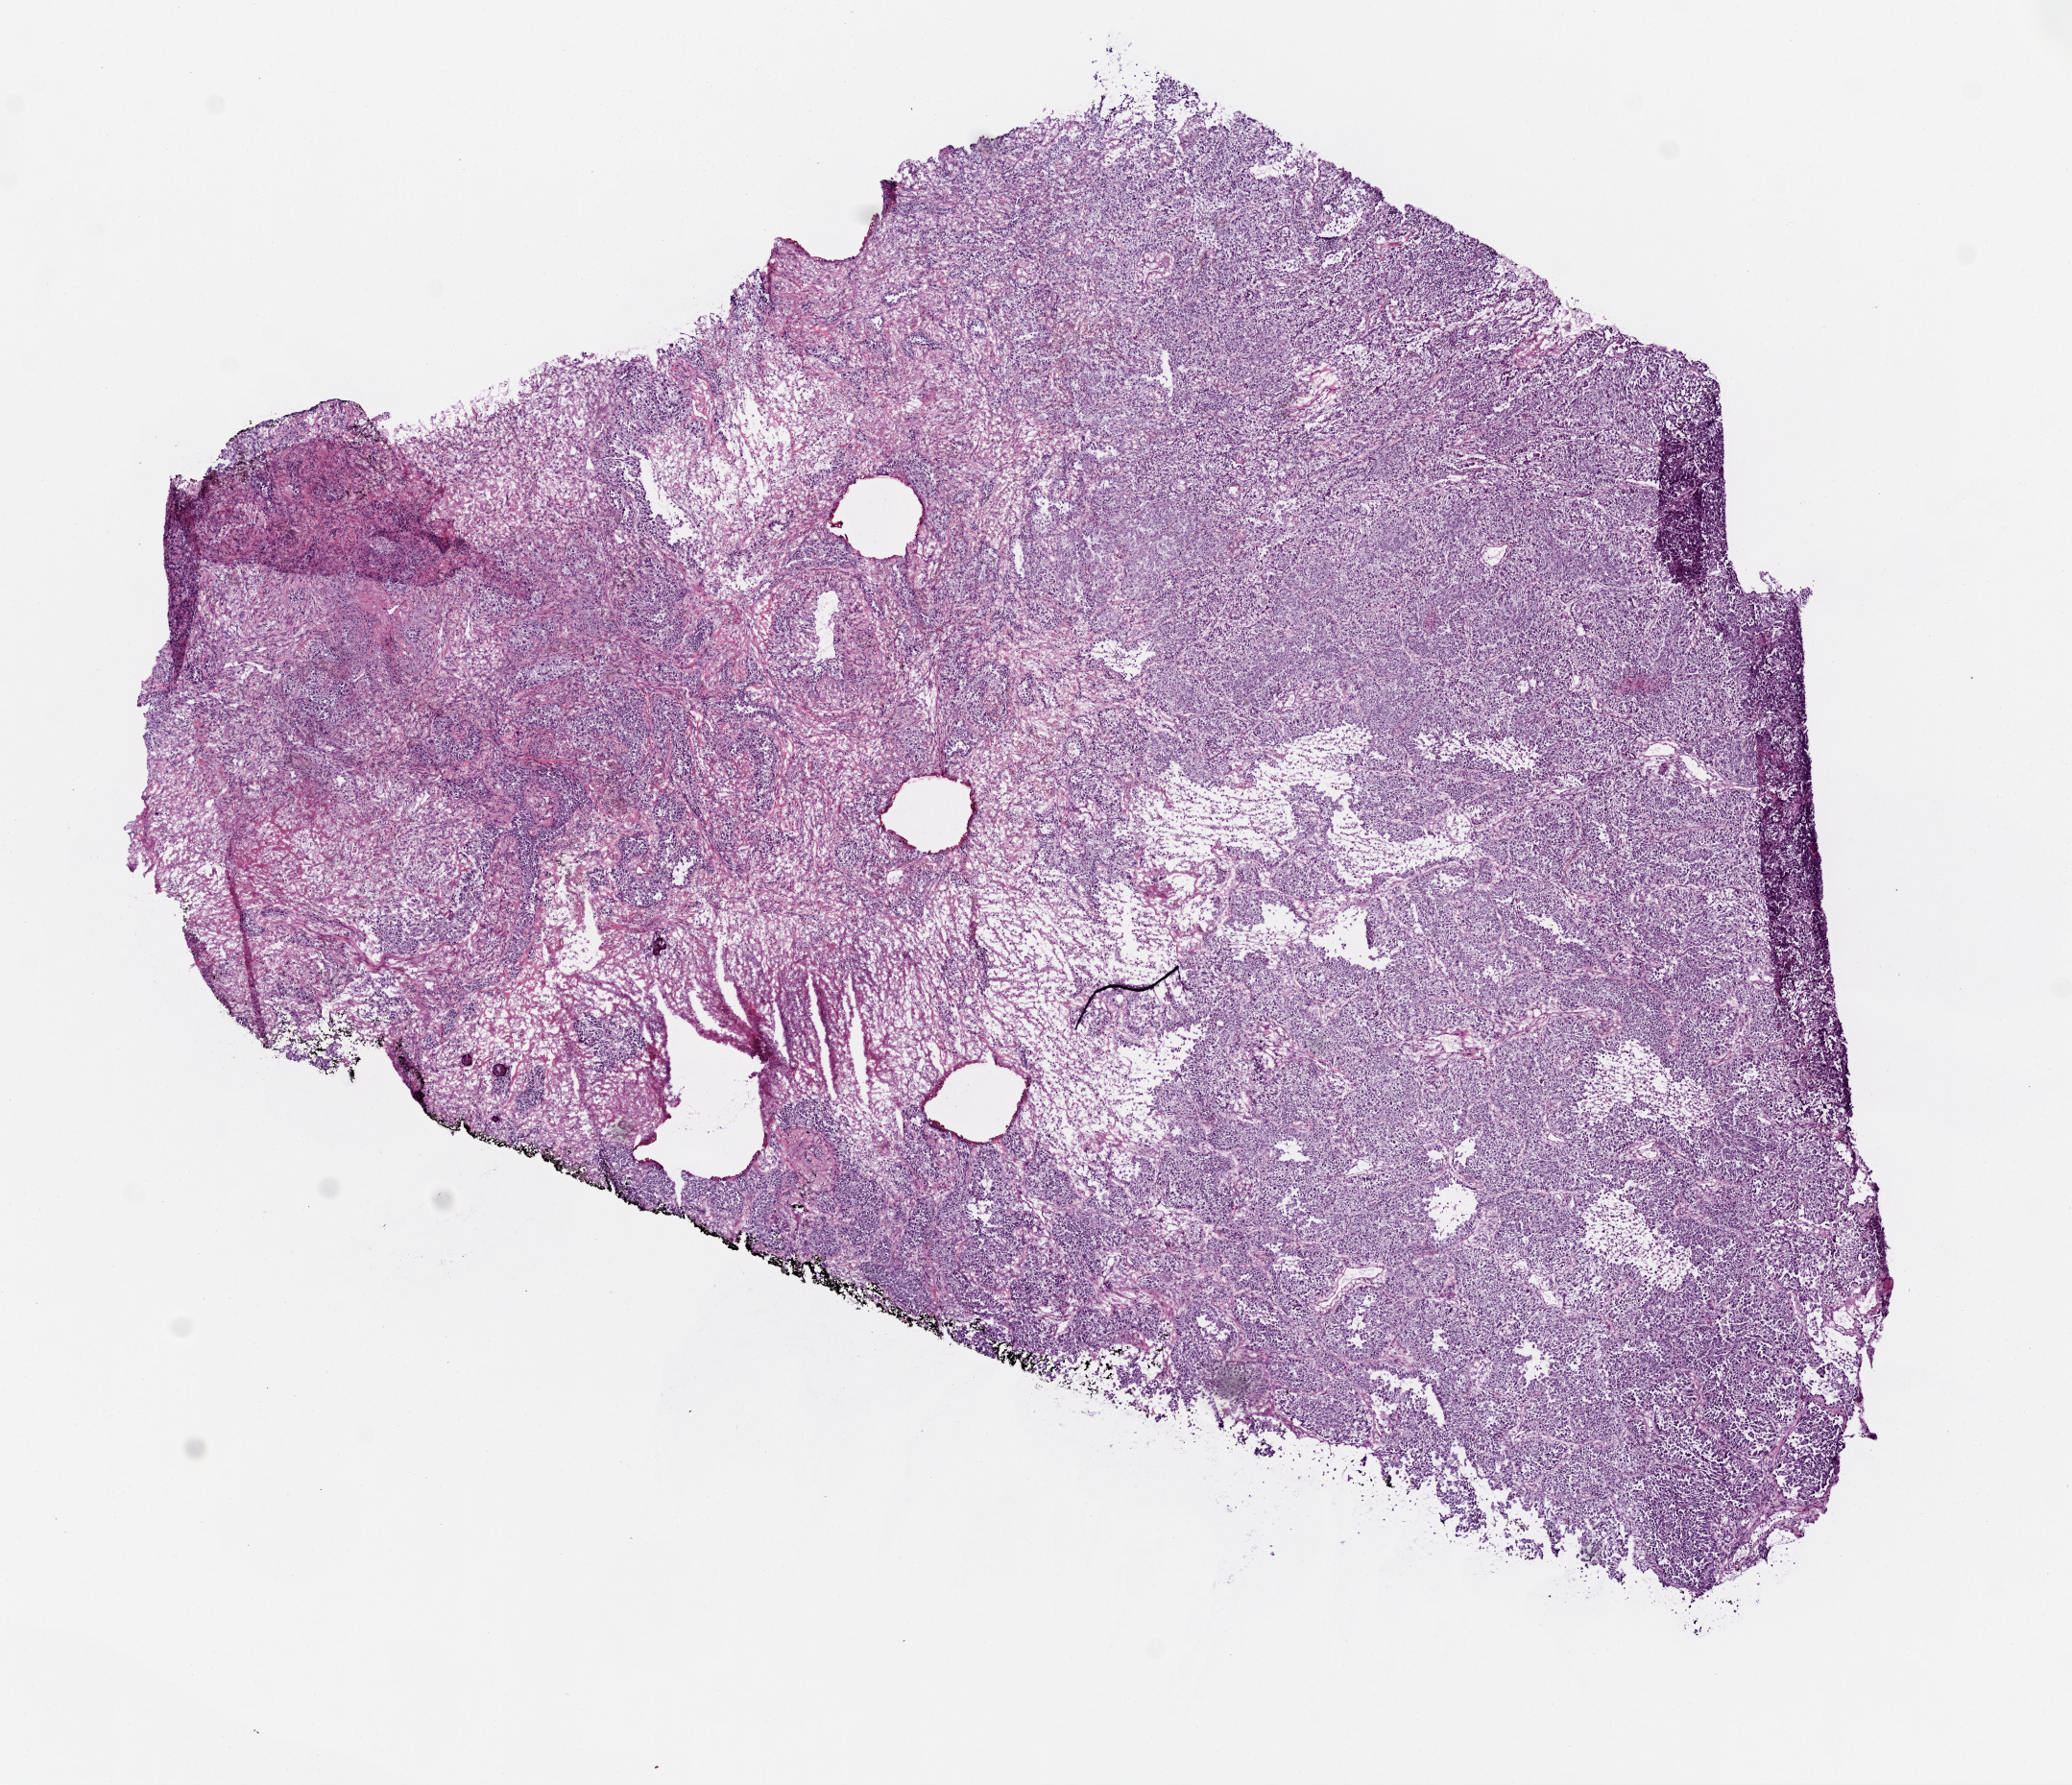
Digitized Hematoxylin and eosin (H&E) stained tissue section (whole slide) — a low-resolution overview of the entire scanned area, about 8.7 x 7.5 mm, frozen section from the top of the tissue portion, sample: primary tumour, lung. Patient: male, age at initial diagnosis 64 years. Composition of this section per pathologist review: tumour cells 9%, tumour nuclei 80%, normal cells 0%, stromal cells 5%, necrosis 5%.
Diagnosis: Adenocarcinoma, NOS. AJCC pathologic stage: IA (7th edition).